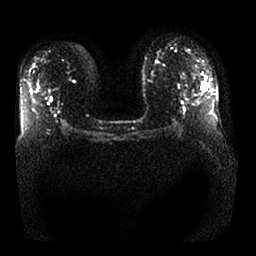
Breast MRI, one axial slice; position 15 of 25 along the scan axis; diffusion-weighted series; image 2 of 4 stored at this slice position (different b-values; order by instance number); 1.5 T; 4 mm slice thickness; 256 × 256 image matrix, field of view 360 × 360 mm. Female patient.
Annotated regions visible in this slice (manually delineated by an expert):
- tumour on diffusion-weighted imaging: bounding box [x1, y1, x2, y2] px = [201, 82, 206, 91]